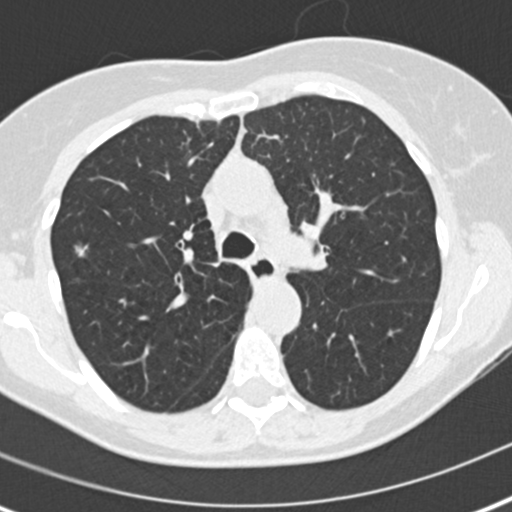
Chest CT (low-dose screening protocol), one axial image; second annual screen; lung window (W 1500 / L -600 HU); 2 mm slice thickness; slice 65 of 186 in the series. Female, age 60 years at enrolment. Current smoker at enrolment.
Lesion marked by an expert reader, box from (x=58, y=231) to (x=101, y=273) px. Reader record for this screening exam (exam-level; its link to the box is not recorded): non-calcified nodule or mass ≥4 mm, right upper lobe, 8 × 6 mm, spiculated (stellate) margins, soft tissue attenuation, pre-existing on the prior screen: no. Participant outcome: lung cancer diagnosed 511 days after this screen — bronchiolo-alveolar adenocarcinoma, NOS, right upper lobe, well differentiated (G1), stage IA (AJCC 6th edition), 11 mm at pathology.